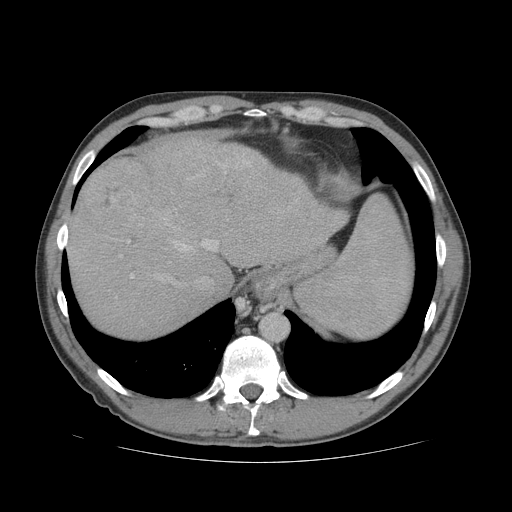
Contrast-enhanced abdominal CT (liver protocol), one axial slice; position 60 of 81 along the scan axis; 140 kVp; soft-tissue window (W 400 / L 40 HU); 2.5 mm slice thickness; 512 × 512 image matrix. From the clinical record (not read from this slice): diagnosis: hepatocellular carcinoma (patient treated with transarterial chemoembolisation; whether this scan precedes or follows treatment is not stated here); TNM stage (as recorded): Stage-IVB; Child-Pugh class: B; tumour differentiation: well differentiated; tumour nodularity: multinodular.
Outlined on this slice (semi-automatically segmented with operator editing):
- abdominal aorta: bounding box (x1, y1, x2, y2) in pixels: (261, 314, 288, 339)
- liver parenchyma outside the tumour (the mass and vessels are separate outlines, so this box may not span the whole liver): (66, 136, 348, 338)
- mass: (80, 158, 153, 241)
- liver vessels: (120, 155, 250, 280)